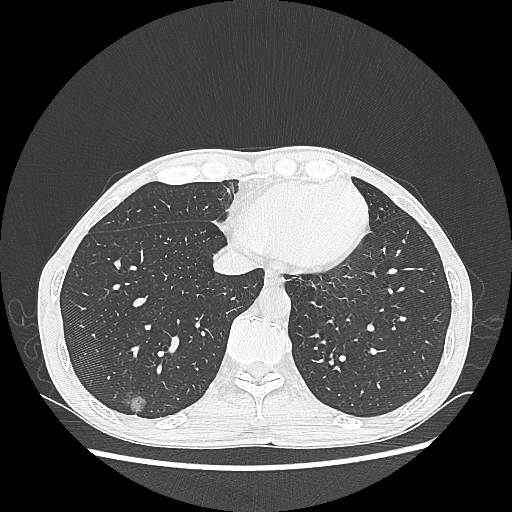
Chest CT, one axial slice. Reconstruction kernel LUNG. Lung window (W 1500 / L -600 HU). 1.25 mm slice thickness. 512 × 512 image matrix. Patient: male, 60 years. Case-level facts recorded for this patient, not image findings: clinical TNM (as recorded): T1c N0 M0; histopathological grade: G2.
Structures marked on this image (rectangle marked by the reading radiologist):
- lung tumour (recorded histology: adenocarcinoma): bounding box <119,383,150,421> (left, top, right, bottom; pixels)